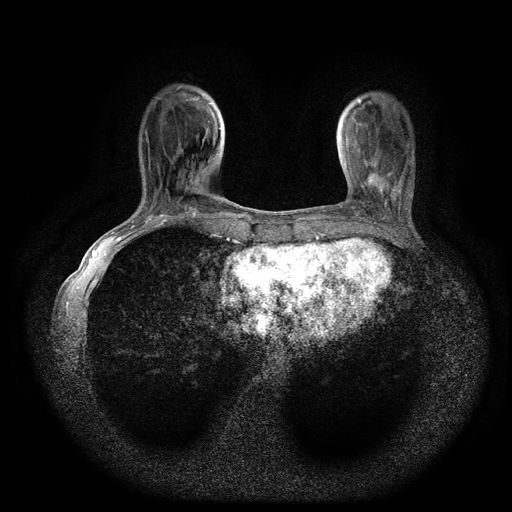
Breast MRI (dynamic contrast-enhanced, multi-phase), one axial slice; position 28 of 116 along the scan axis; dynamic contrast-enhanced series, time point 2 of 5 at this slice position (early post-contrast); 1.5 T; TE 2.7 ms, TR 5.4 ms; 2 mm slice thickness; 512 × 512 image matrix, field of view 330 × 330 mm. Patient: female, 49 years.
Outlined on this slice (semi-automatically segmented with operator editing):
- breast lesion (labelled 'tumour' in the annotation; benign lesions carry a separate 'benign' label): bounding box (x1, y1, x2, y2) in pixels: (363, 169, 381, 192)